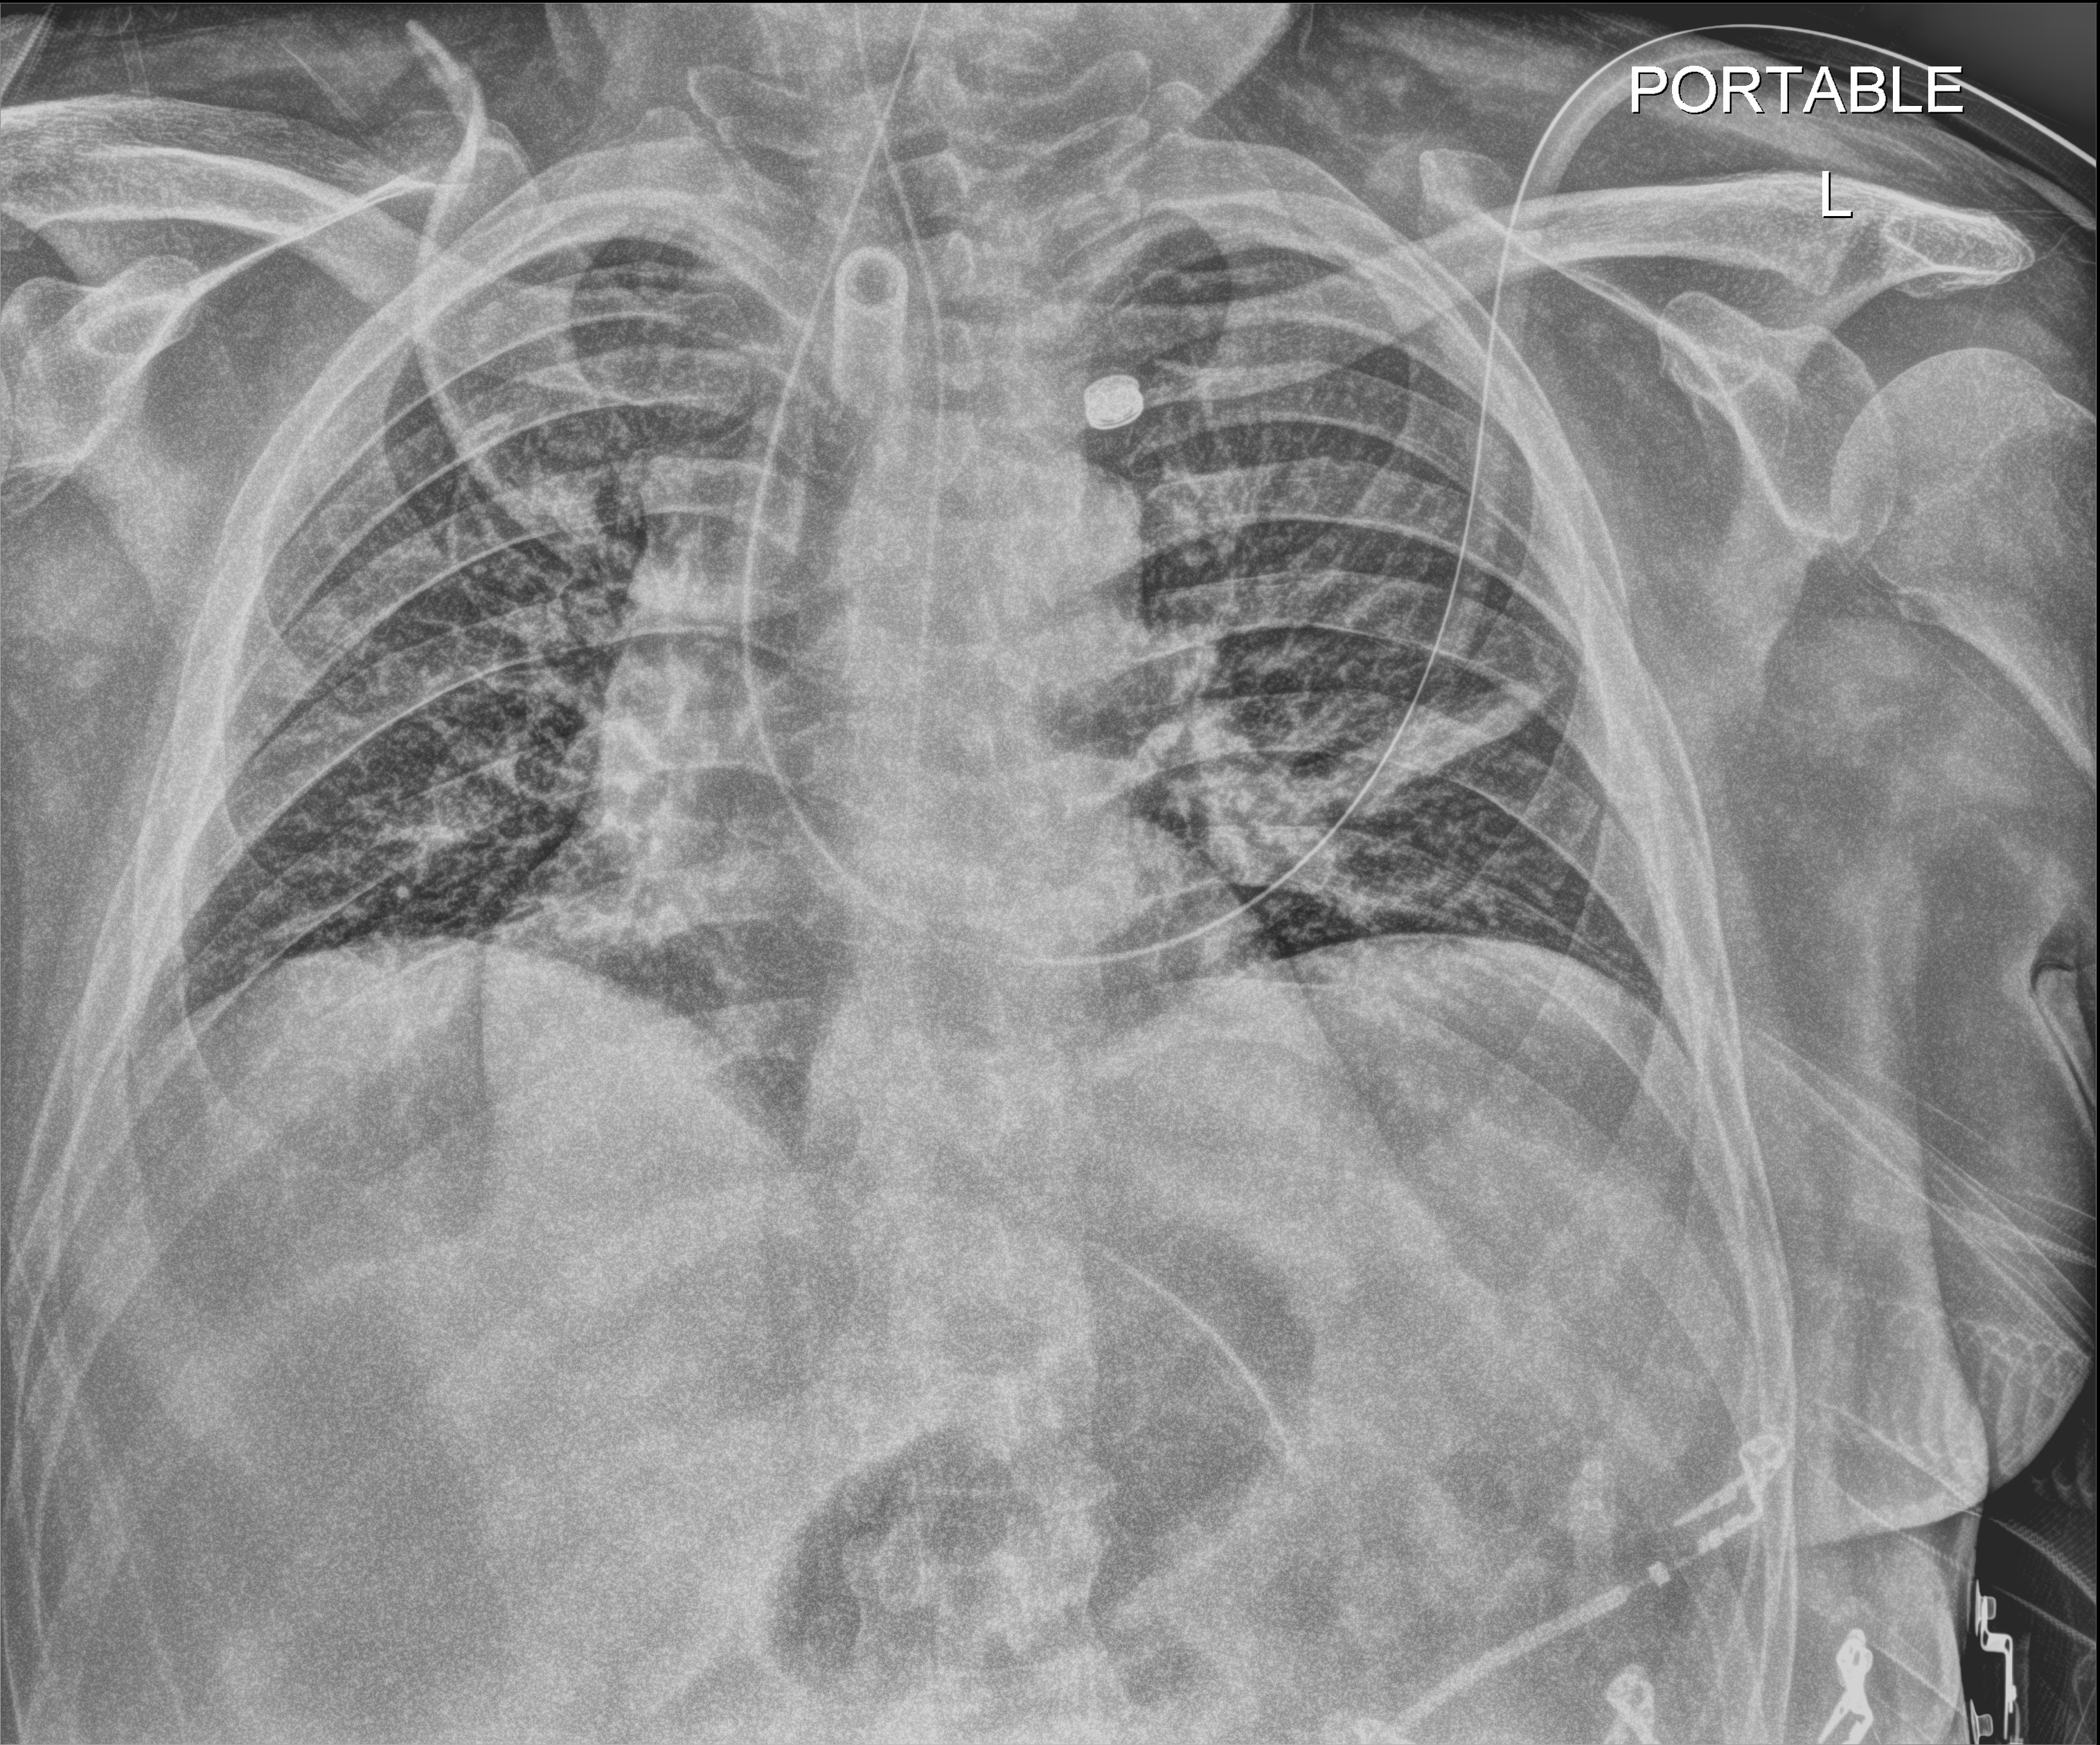
Chest X-ray (portable), anteroposterior (AP) projection. Male patient hospitalised with COVID-19, age 18–59 years.
Admission-level facts for this patient (not findings on this image; timing relative to this image not recorded):
- mechanically ventilated during this hospital stay: yes
- admitted to intensive care during this hospital stay: yes